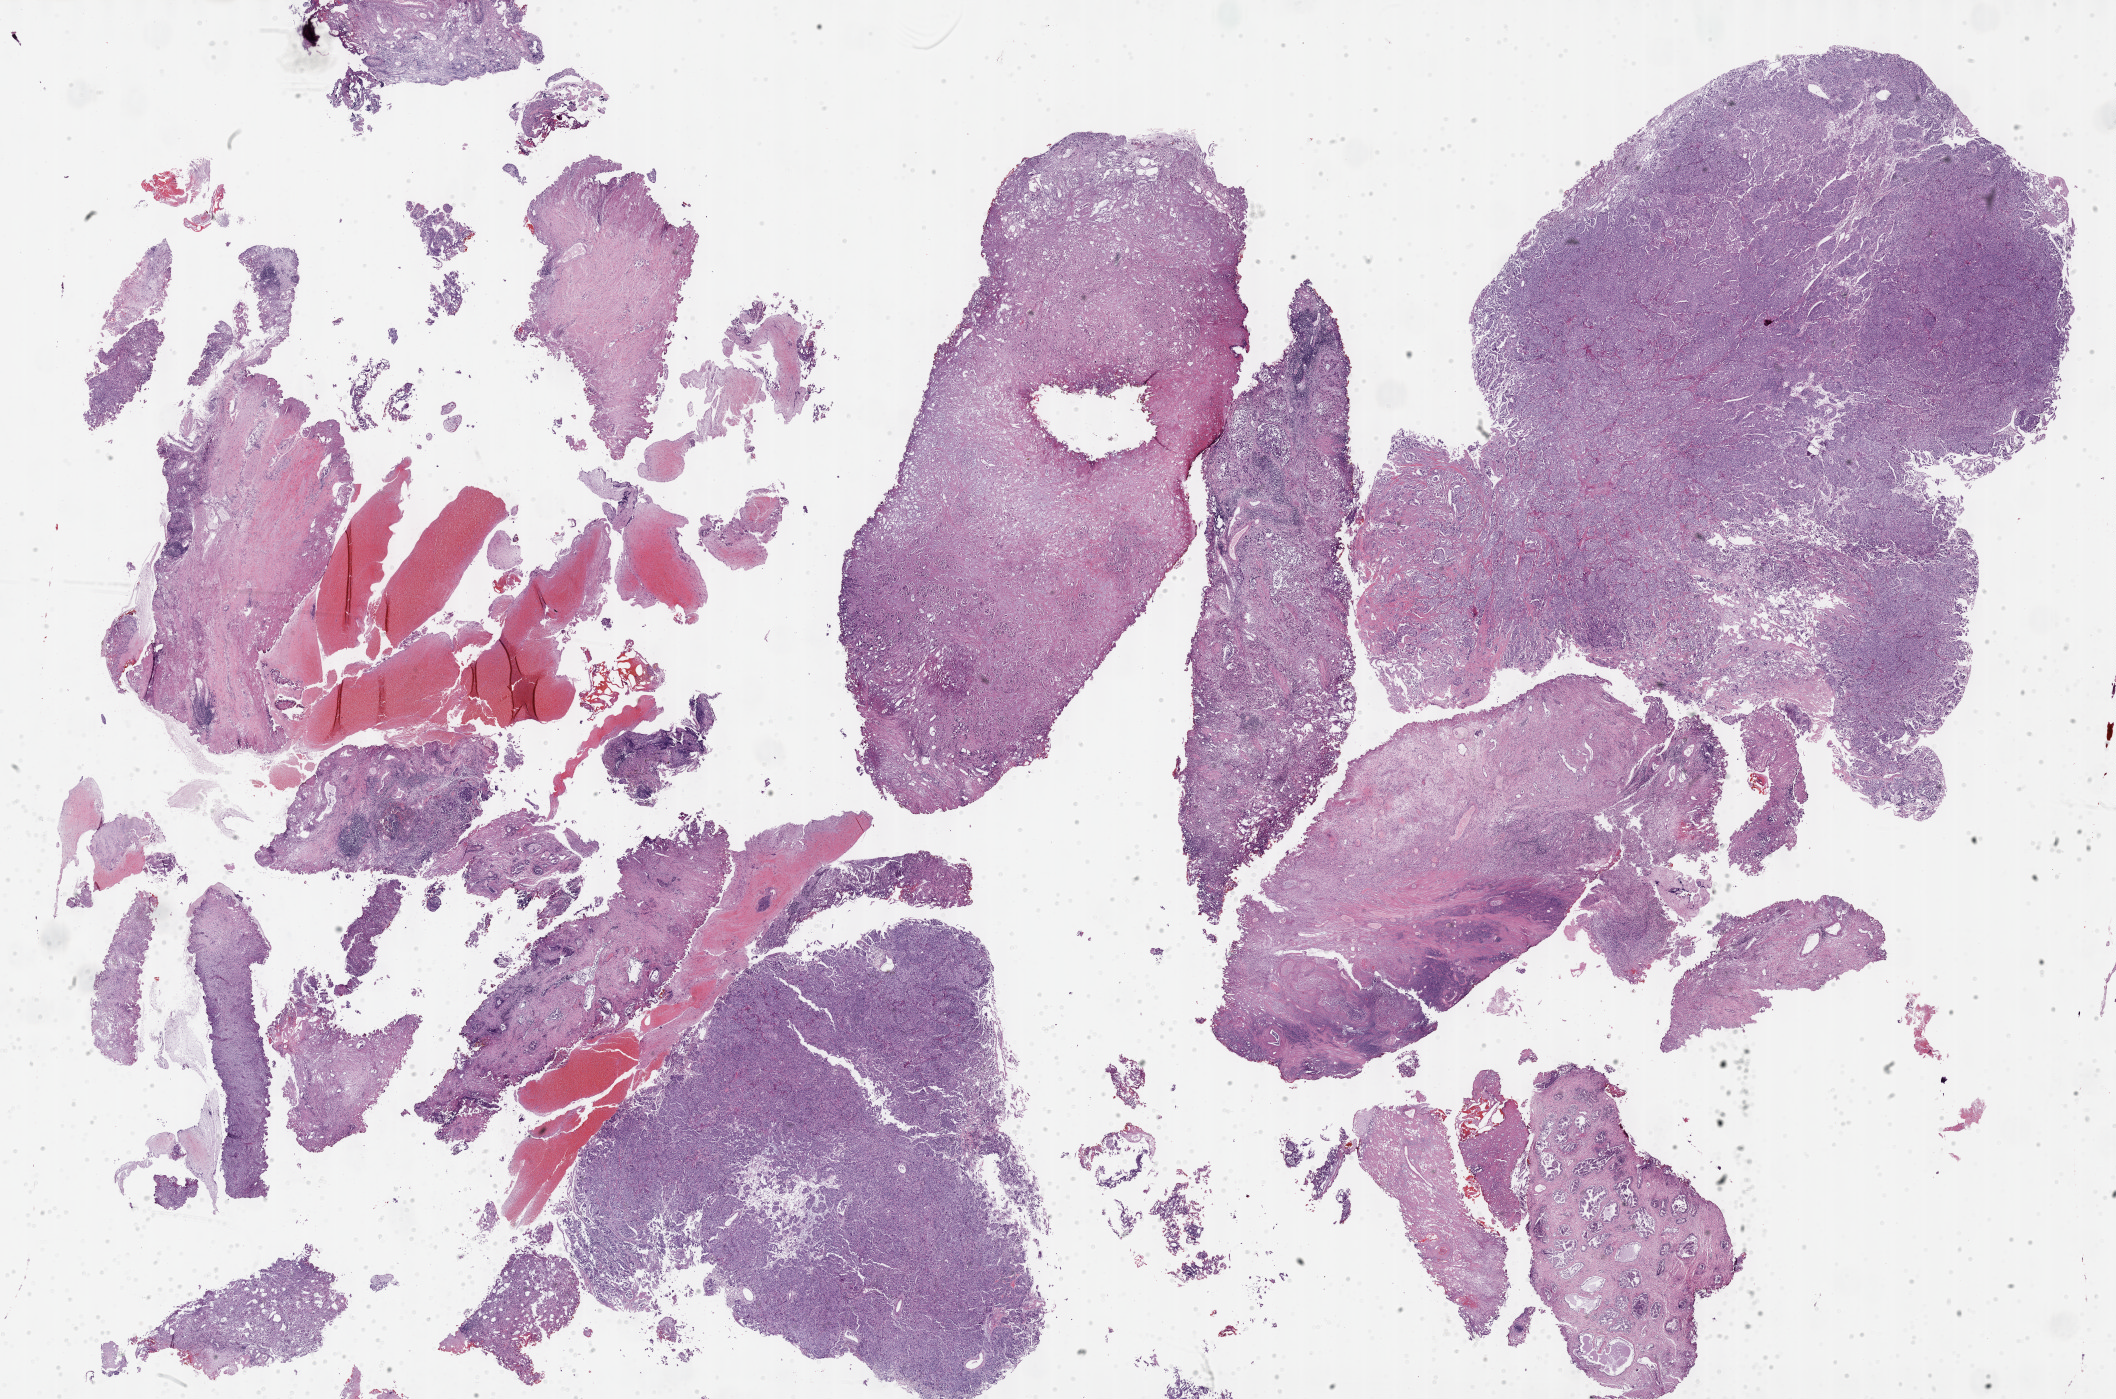
H&E whole-slide image — whole scanned area (about 34.2 x 22.6 mm) shown as a low-resolution overview. FFPE section. Bladder, primary tumour sample. Male patient; age at initial diagnosis 77 years.
Pathologic diagnosis: Transitional cell carcinoma.